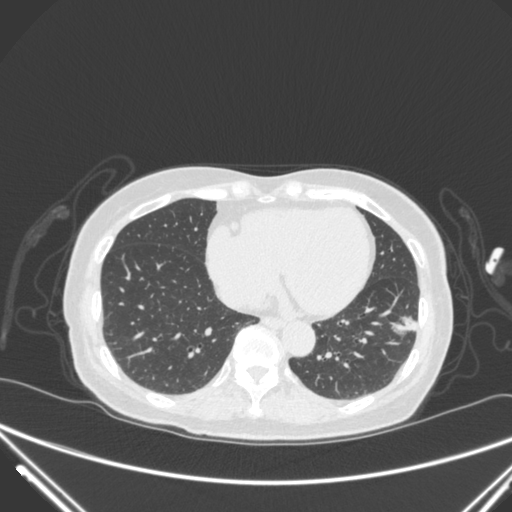
Chest CT, one axial slice. Position 104 of 310 along the scan axis. 120 kVp. Lung window (W 1500 / L -600 HU). 1 mm slice thickness. 512 × 512 image matrix, field of view 377 × 377 mm. Patient: female, 82 years. Case-level facts recorded for this patient, not image findings: clinical TNM (as recorded): T1c N0 M0.
Structures marked on this image (bounding box drawn by a radiologist):
- lung tumour (recorded histology: adenocarcinoma): bounding box <389,315,435,356> (left, top, right, bottom; pixels)